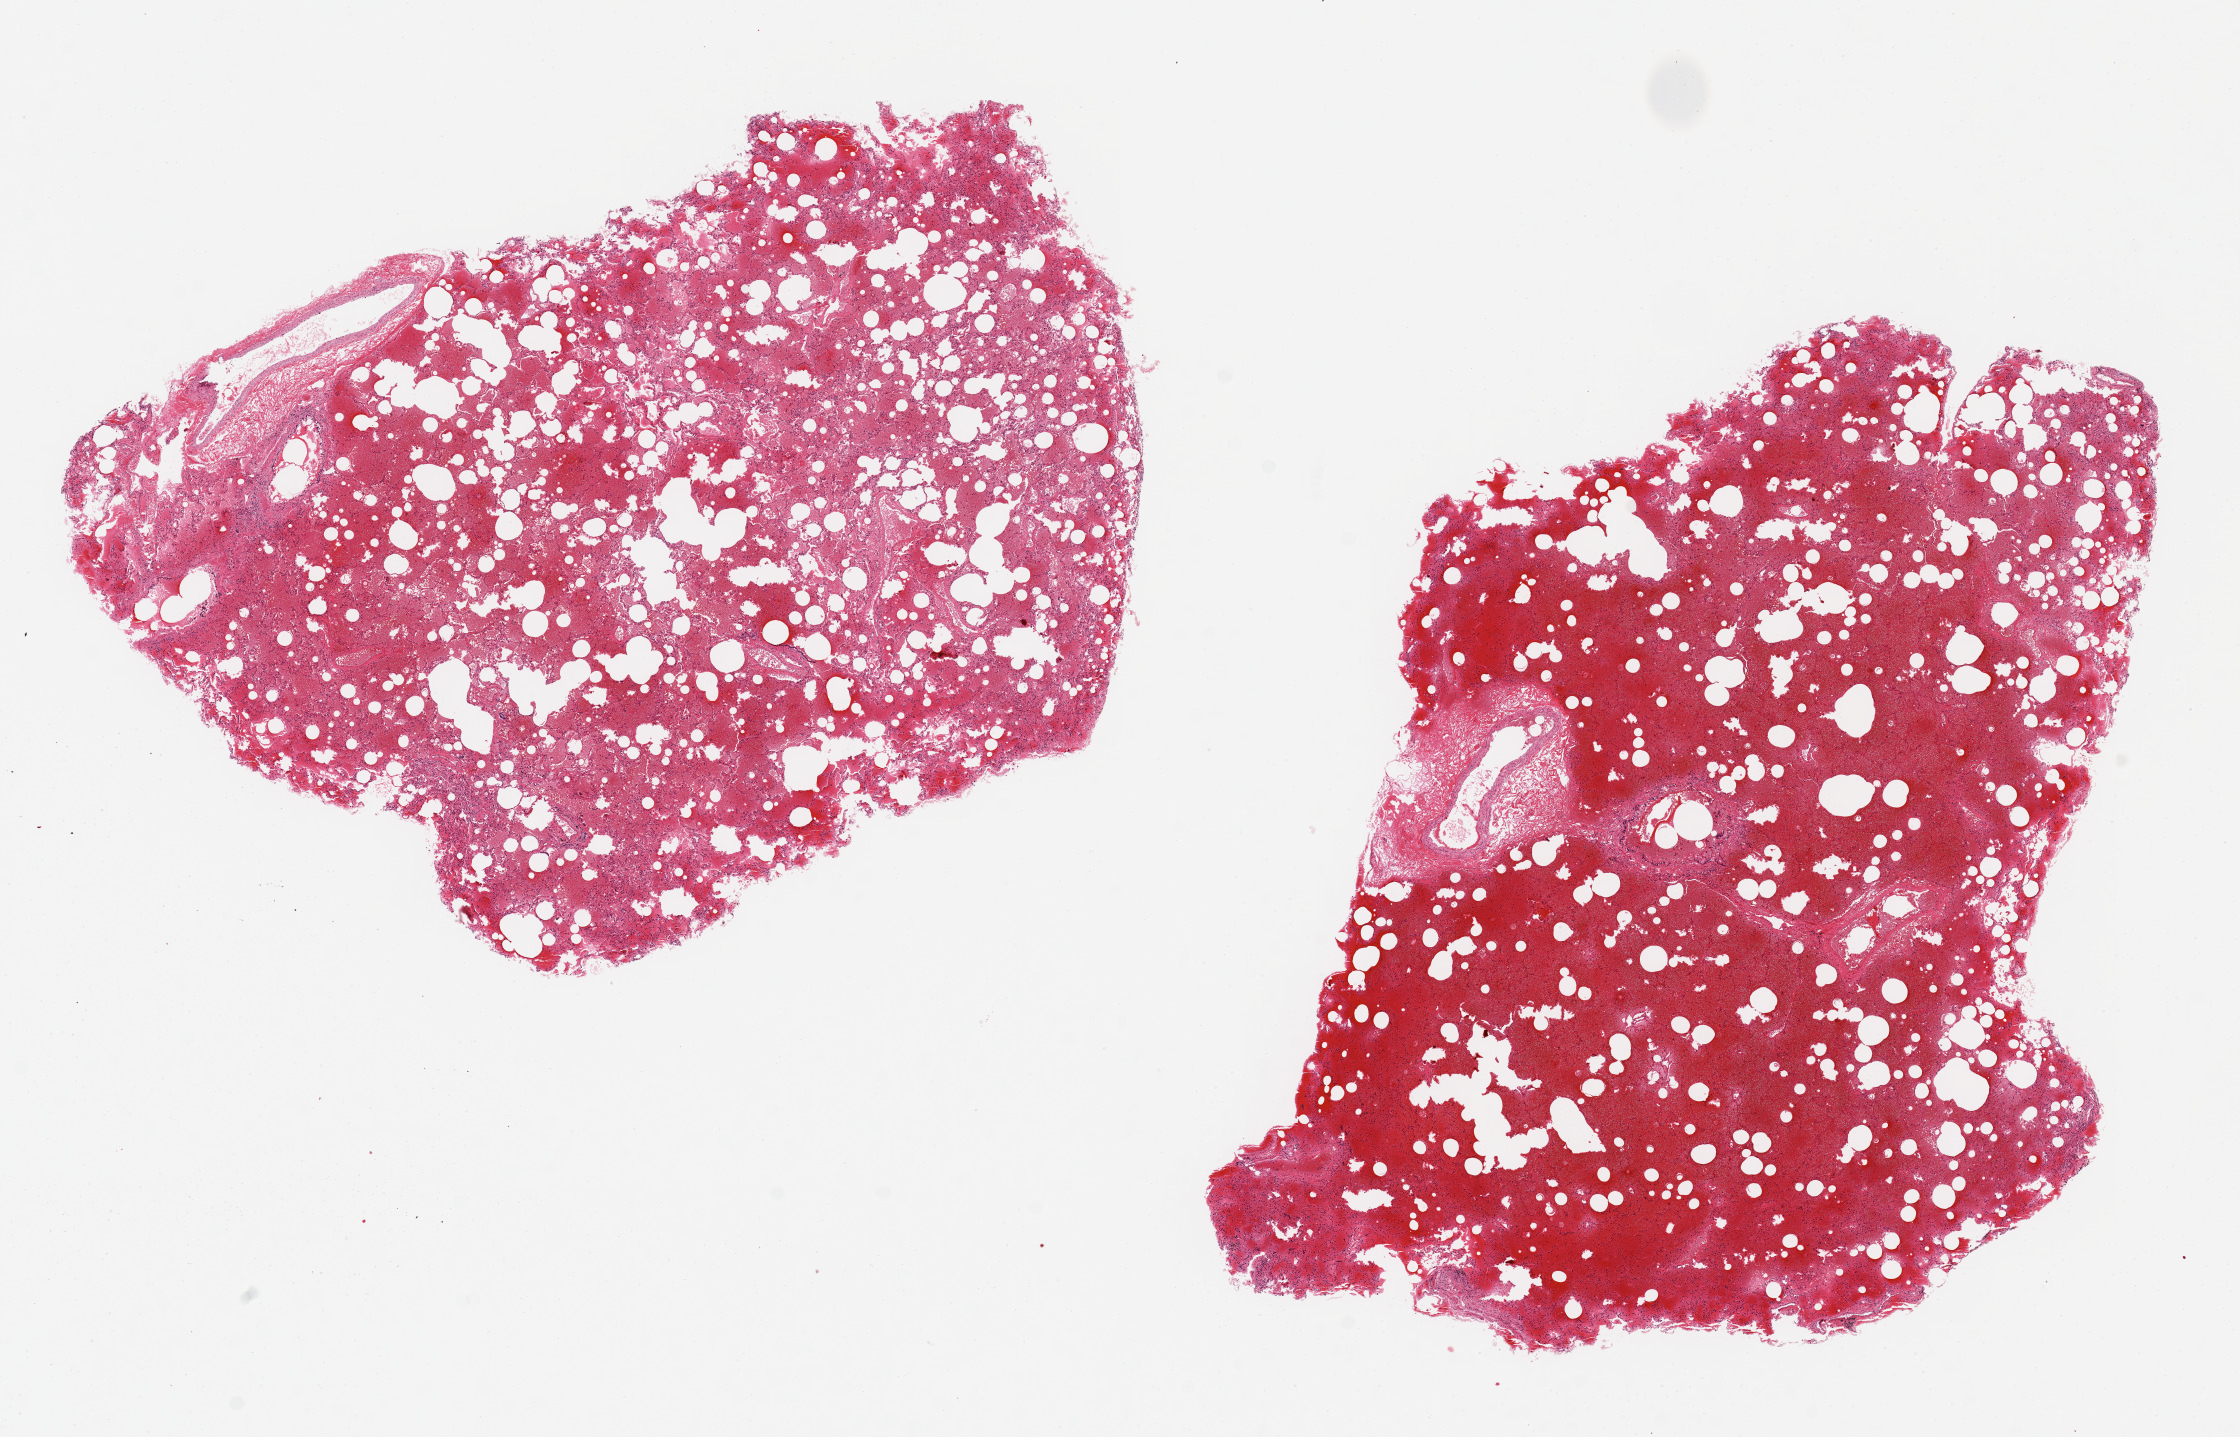
Hematoxylin and eosin (H&E) whole-slide image, a low-resolution overview of the entire scanned area, about 17.7 x 11.4 mm. PAXgene-fixed, paraffin-embedded tissue. Target tissue: lung. Donor tissue sample. Male donor.
Pathologist's review note for this sample: 2 pieces, 8x5&7x6 mm; extensive recent hemorrhage; no underlying lesion detected.